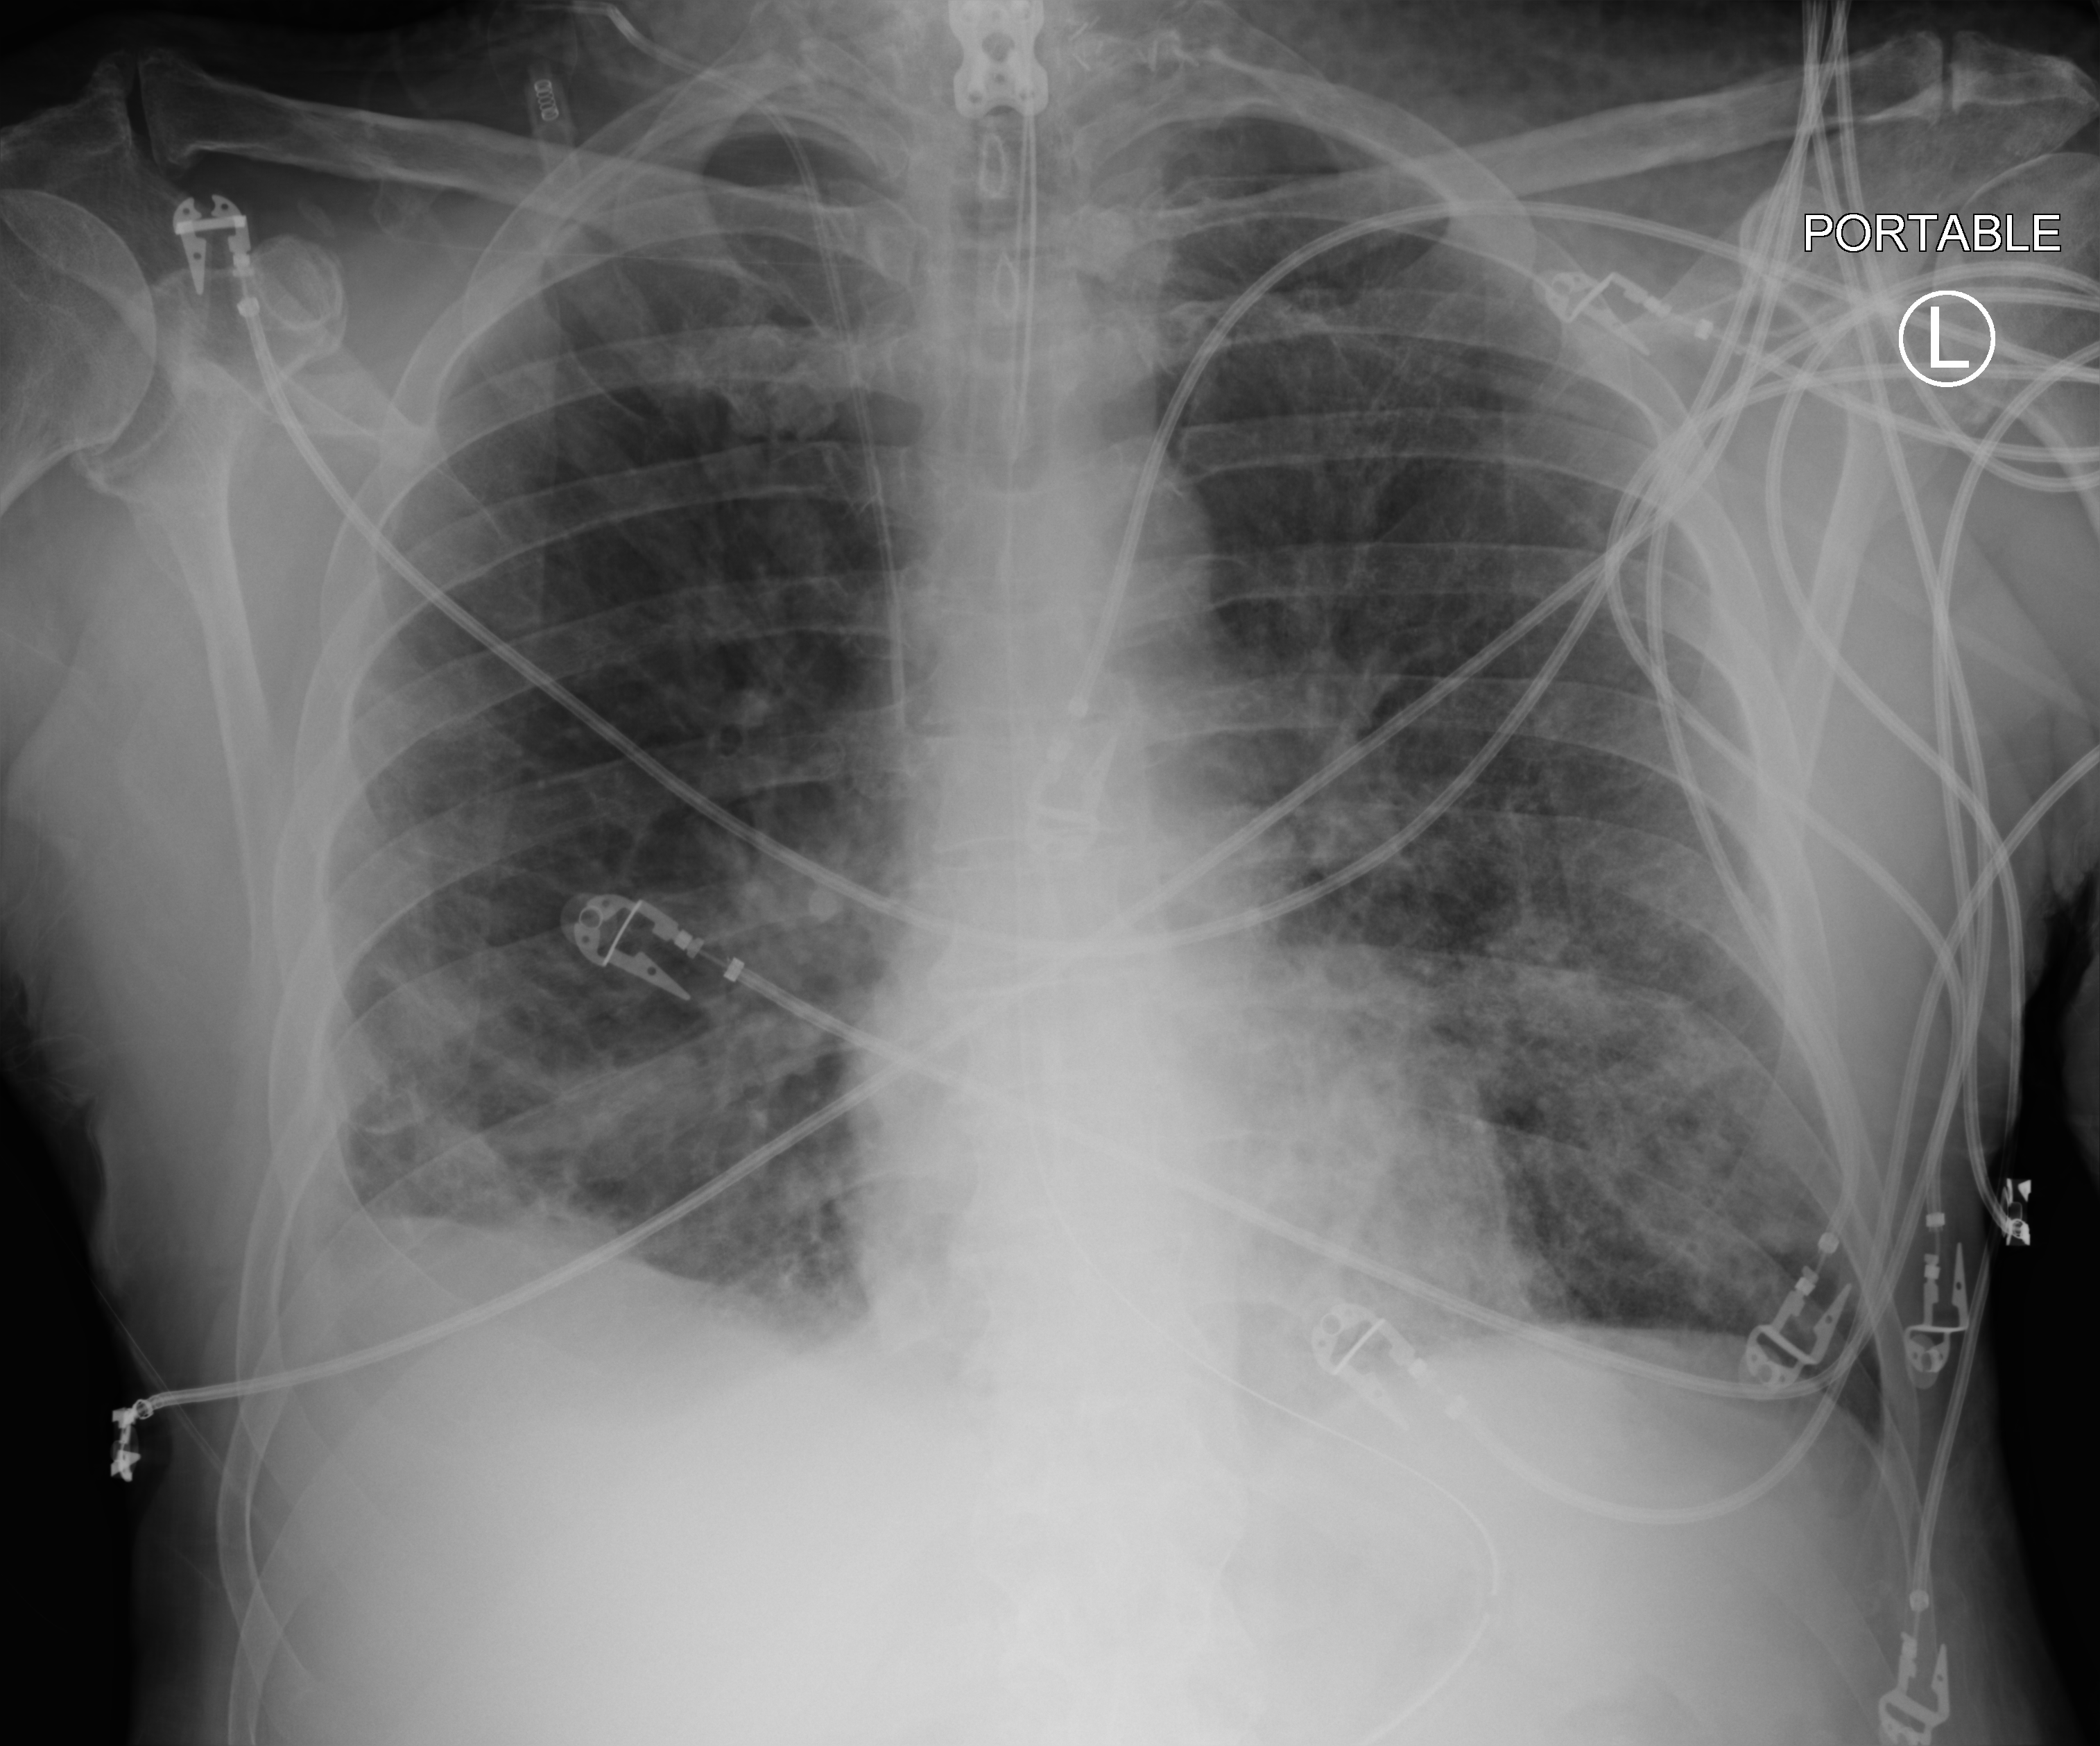
Chest X-ray (portable). Male patient hospitalised with COVID-19, age 60–74 years.
Hospital-stay facts (about this admission, not read from this image; timing relative to this image not recorded):
- mechanically ventilated during this hospital stay: yes
- admitted to intensive care during this hospital stay: yes
- length of hospital stay: 43 days